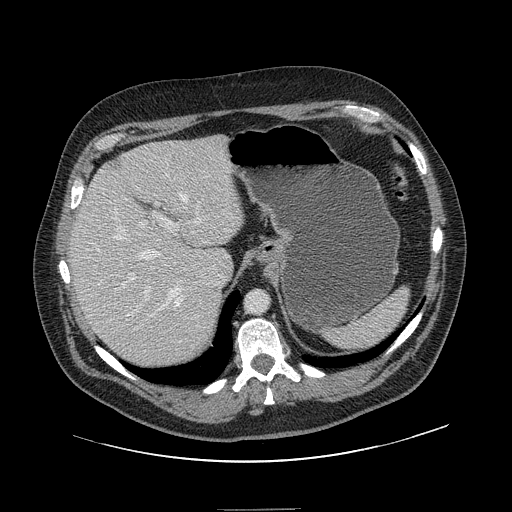
Contrast-enhanced abdominal CT, one axial slice. Slice 110 of 154 in the series (ordered by position). 120 kVp. Soft-tissue window (W 400 / L 40 HU). 2.5 mm slice thickness. 512 × 512 image matrix. Male patient, age 61 years. From the clinical record (not read from this slice): diagnosis: colorectal cancer liver metastases, imaged before liver resection; multiple liver metastases: yes; largest metastasis: 2.6 cm; chemotherapy before resection: no.
Annotated regions visible in this slice (manually delineated by an expert):
- hepatic veins: bounding box <114,193,188,316> (left, top, right, bottom; pixels)
- liver: <71,137,243,368>
- planned liver remnant (the part of the liver to remain after resection): <71,144,243,358>
- portal vein (with intrahepatic branches): <121,203,202,316>